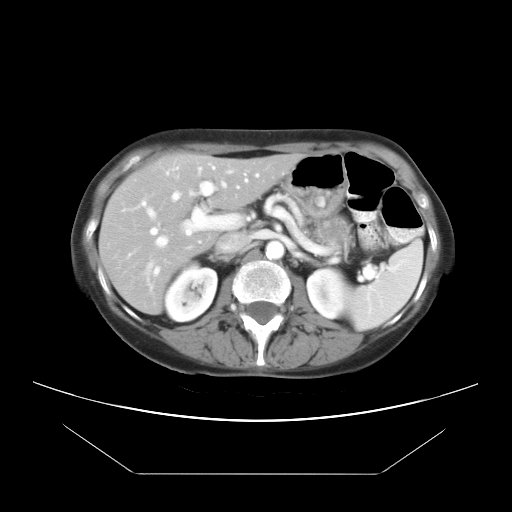
Contrast-enhanced abdominal CT, one axial slice. 120 kVp. Intravenous contrast given. Soft-tissue window (W 400 / L 40 HU). 7.5 mm slice thickness. 512 × 512 image matrix, field of view 392 × 392 mm. Female patient, age 72 years. Case-level facts recorded for this patient, not image findings: diagnosis: colorectal cancer liver metastases, imaged before liver resection; multiple liver metastases: yes; largest metastasis: 4 cm; chemotherapy before resection: yes.
Structures marked on this image (manually delineated by an expert):
- hepatic veins: bounding box [x1, y1, x2, y2] px = [155, 167, 247, 248]
- liver: [102, 154, 298, 312]
- planned liver remnant (the part of the liver to remain after resection): [102, 154, 298, 282]
- portal vein (with intrahepatic branches): [140, 181, 227, 274]